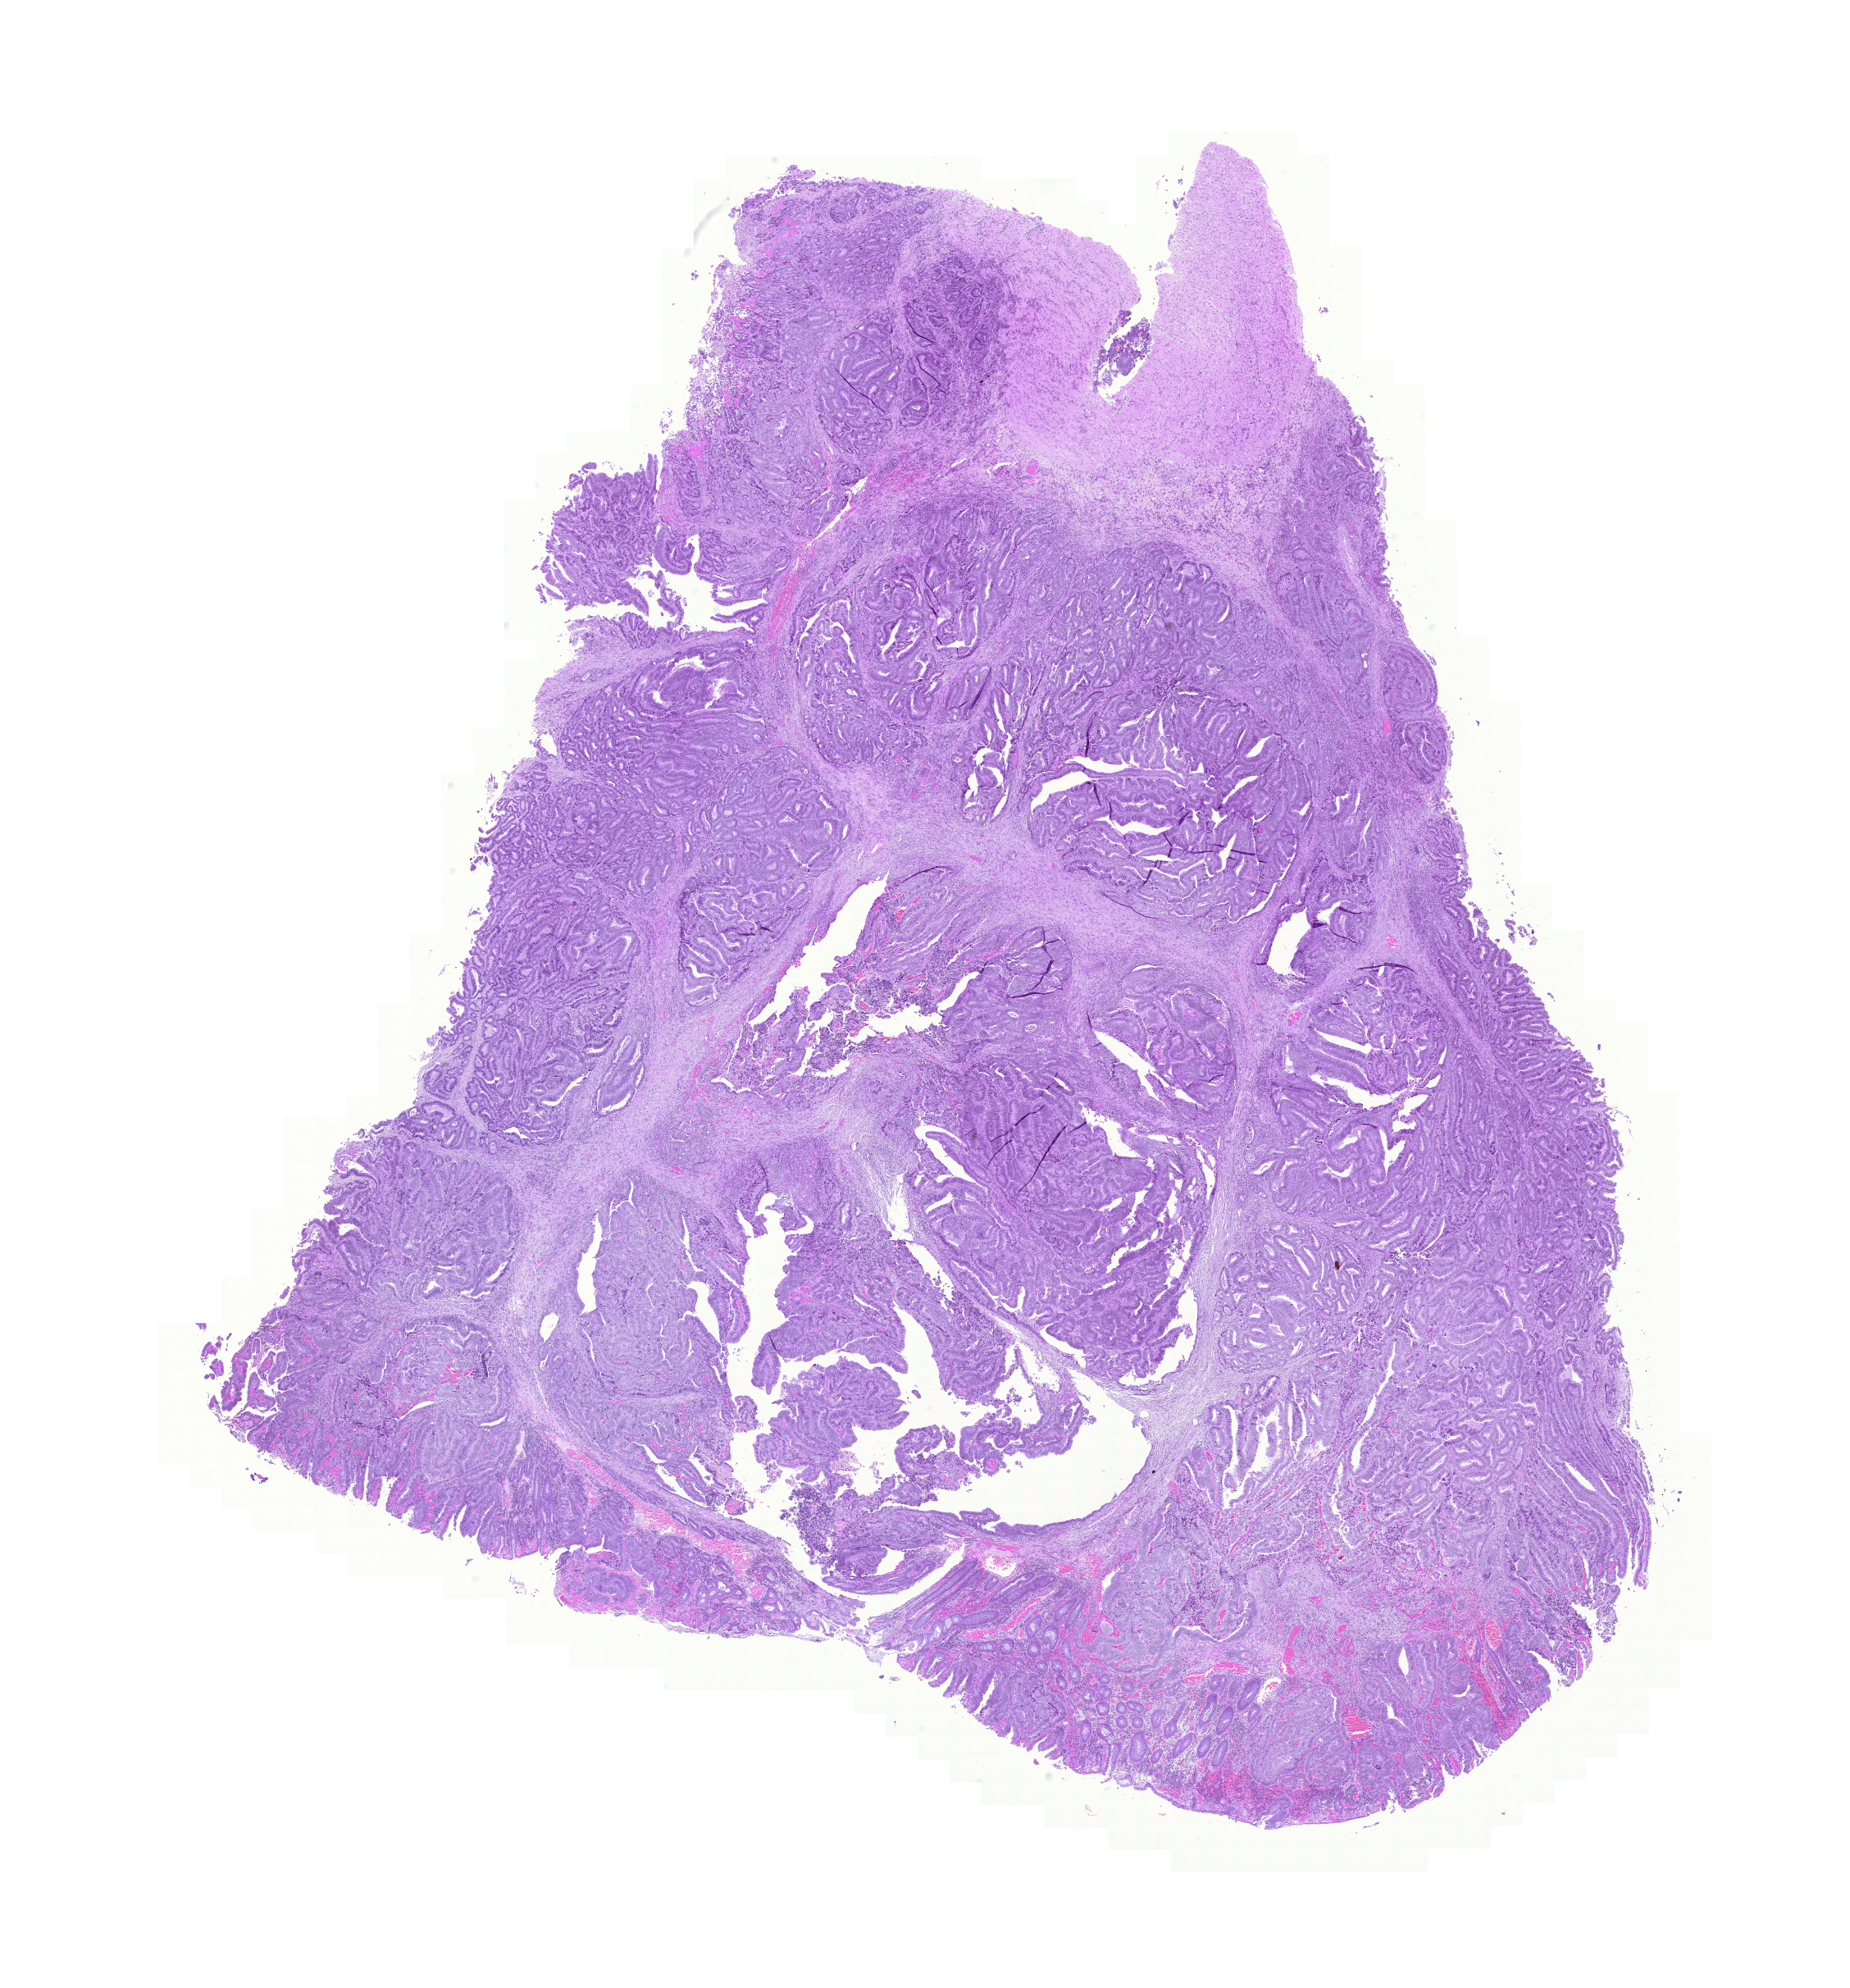
H&E-stained whole-slide image, low-resolution overview of the scanned area, about 16.8 x 18.0 mm (from a 20x scan); formalin-fixed paraffin-embedded (FFPE) diagnostic section; rectum, primary tumour sample. Patient: female, age at initial diagnosis 67 years.
- AJCC pathologic stage: II (5th edition)
- lymph nodes positive (case pathology): 0 of 20 examined
- diagnosis: Adenocarcinoma, NOS